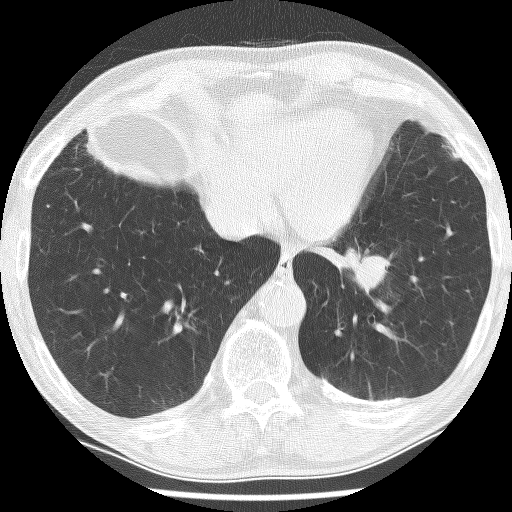
Low-dose screening chest CT, one axial slice. Slice 43 of 226 in the series (ordered by position). 120 kVp. Lung window (W 1500 / L -600 HU). 2.5 mm slice thickness. 512 × 512 image matrix, field of view 320 × 320 mm.
Structures marked on this image (expert manual segmentation):
- lesion 1 (tumor, lower lobe of left lung): bounding box (x1, y1, x2, y2) in pixels: (341, 248, 391, 296)